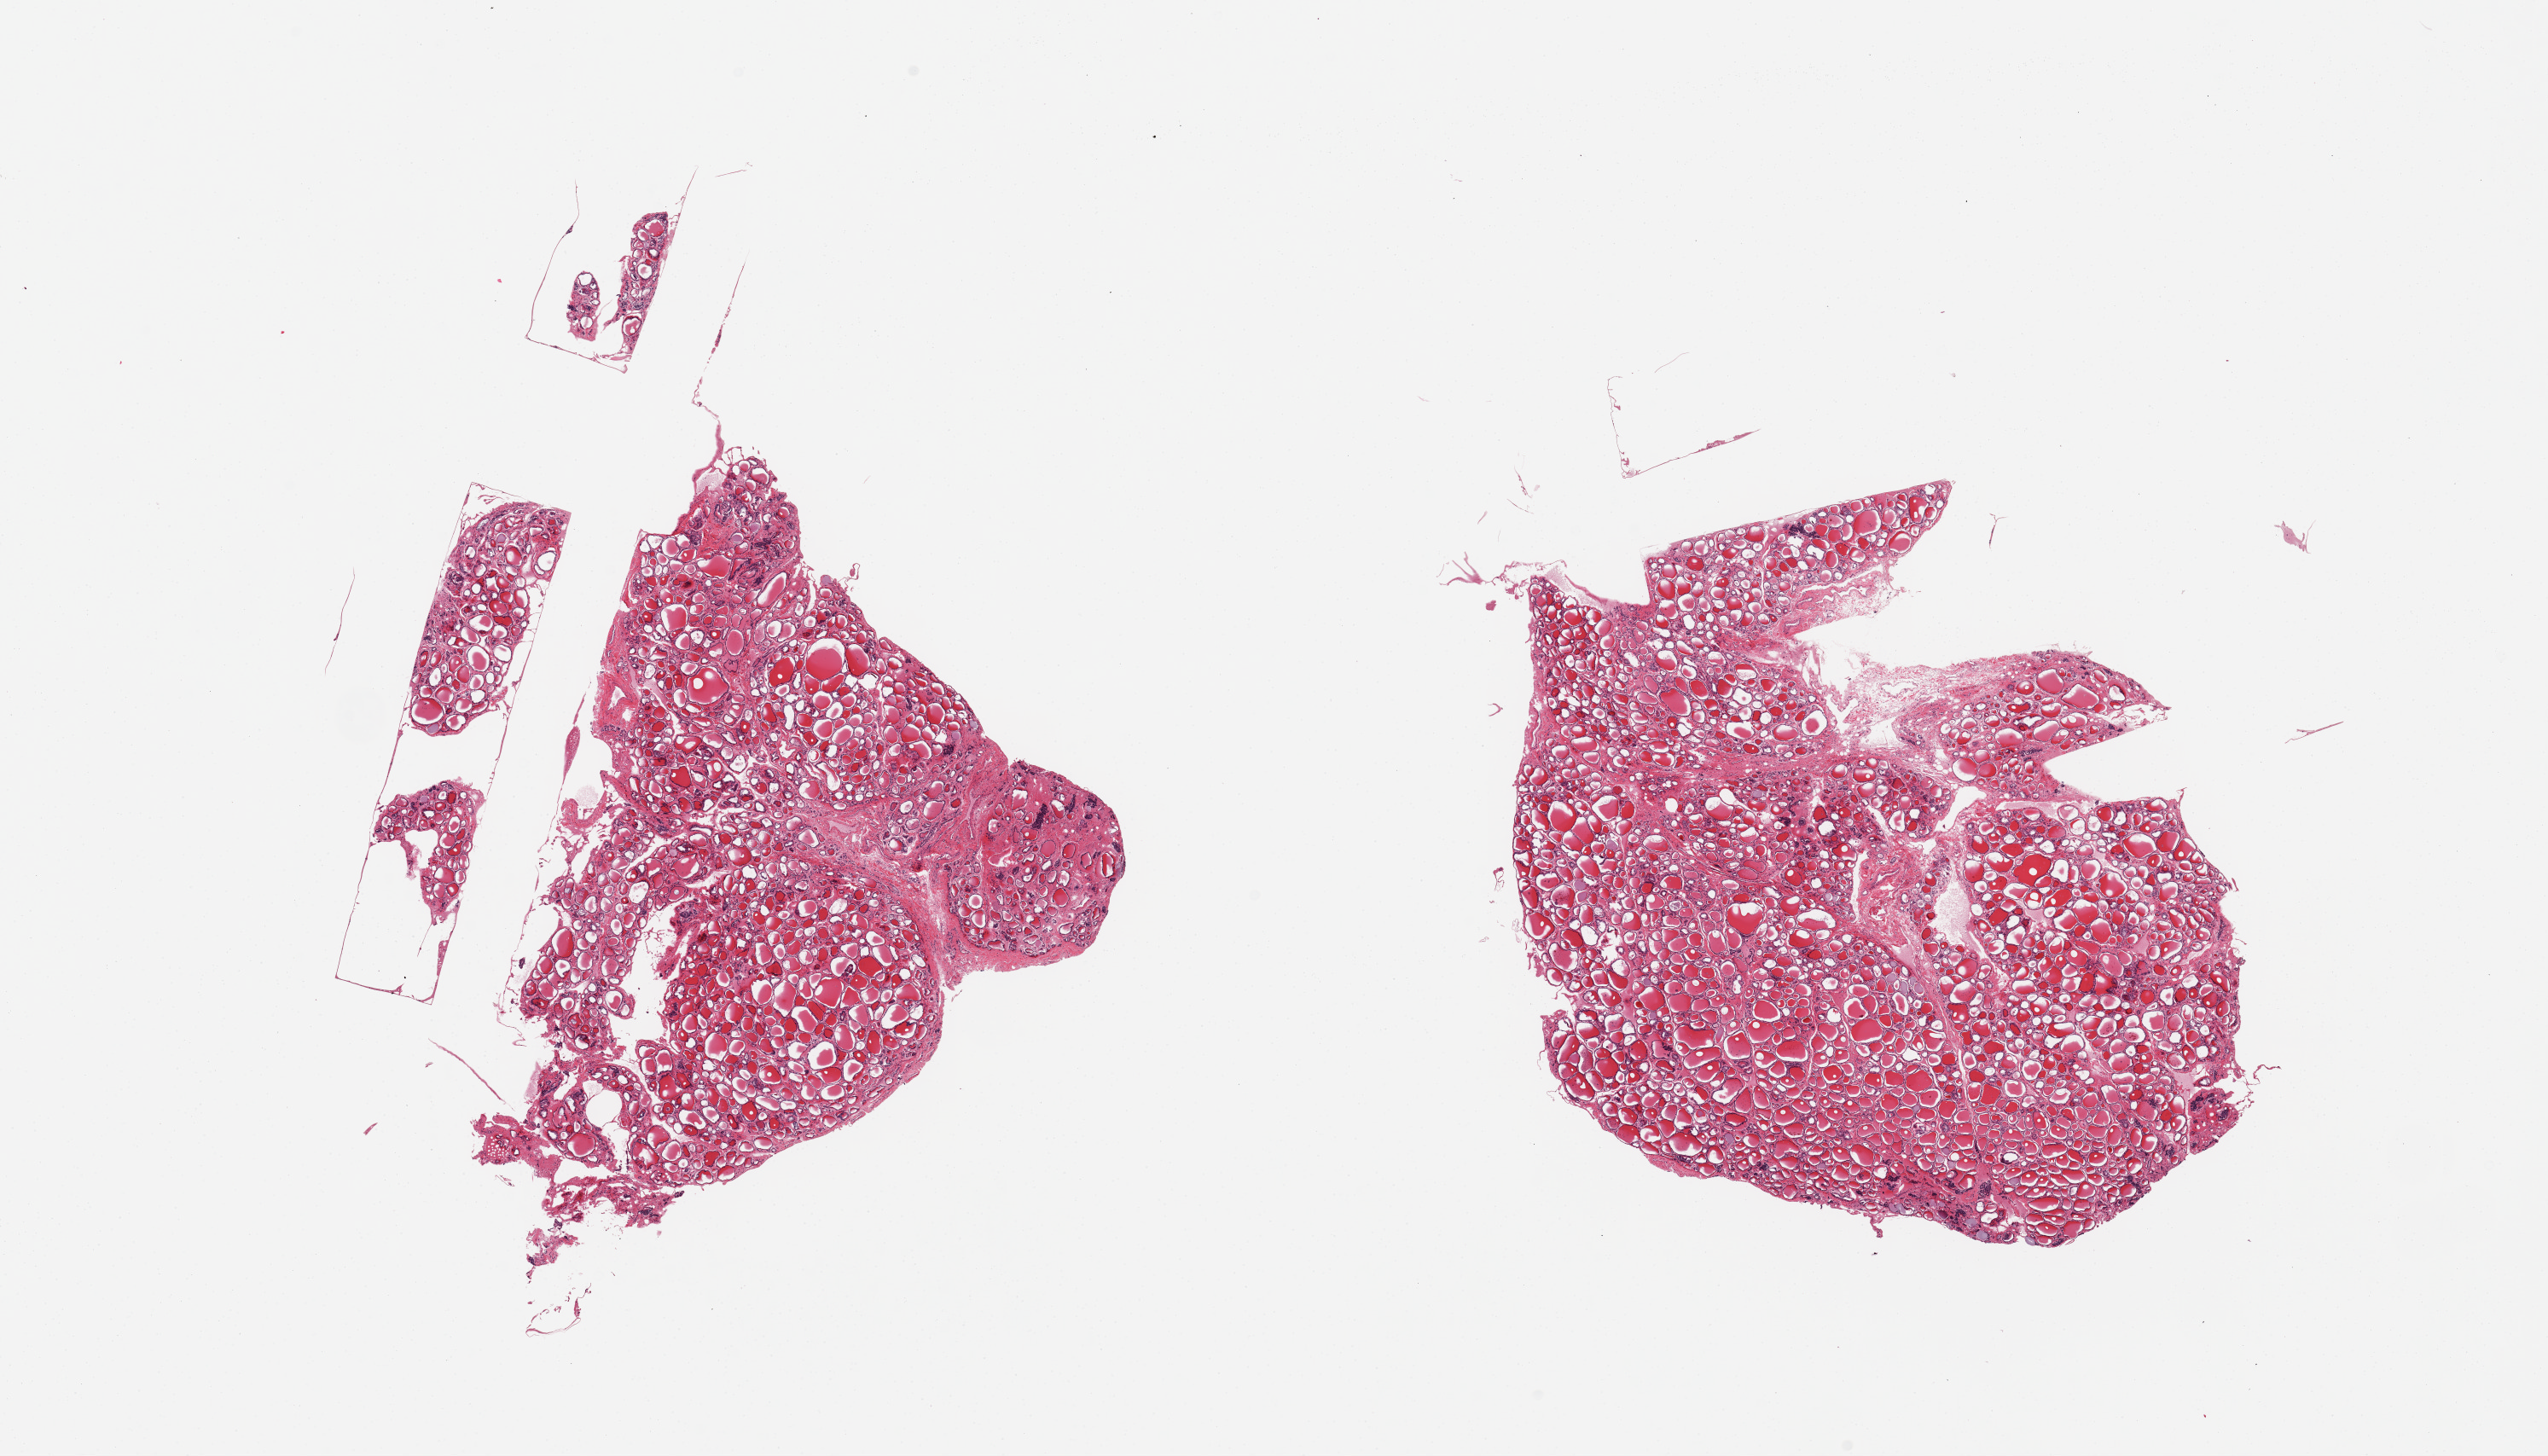
Whole-slide image, haematoxylin and eosin stain — shown as a low-resolution overview of the whole scanned area (about 23.6 x 13.5 mm, from a 20x scan), PAXgene-fixed, paraffin-embedded tissue, section of thyroid (target tissue), tissue donor sample.
* reviewer comment on this tissue sample: 2 pieces